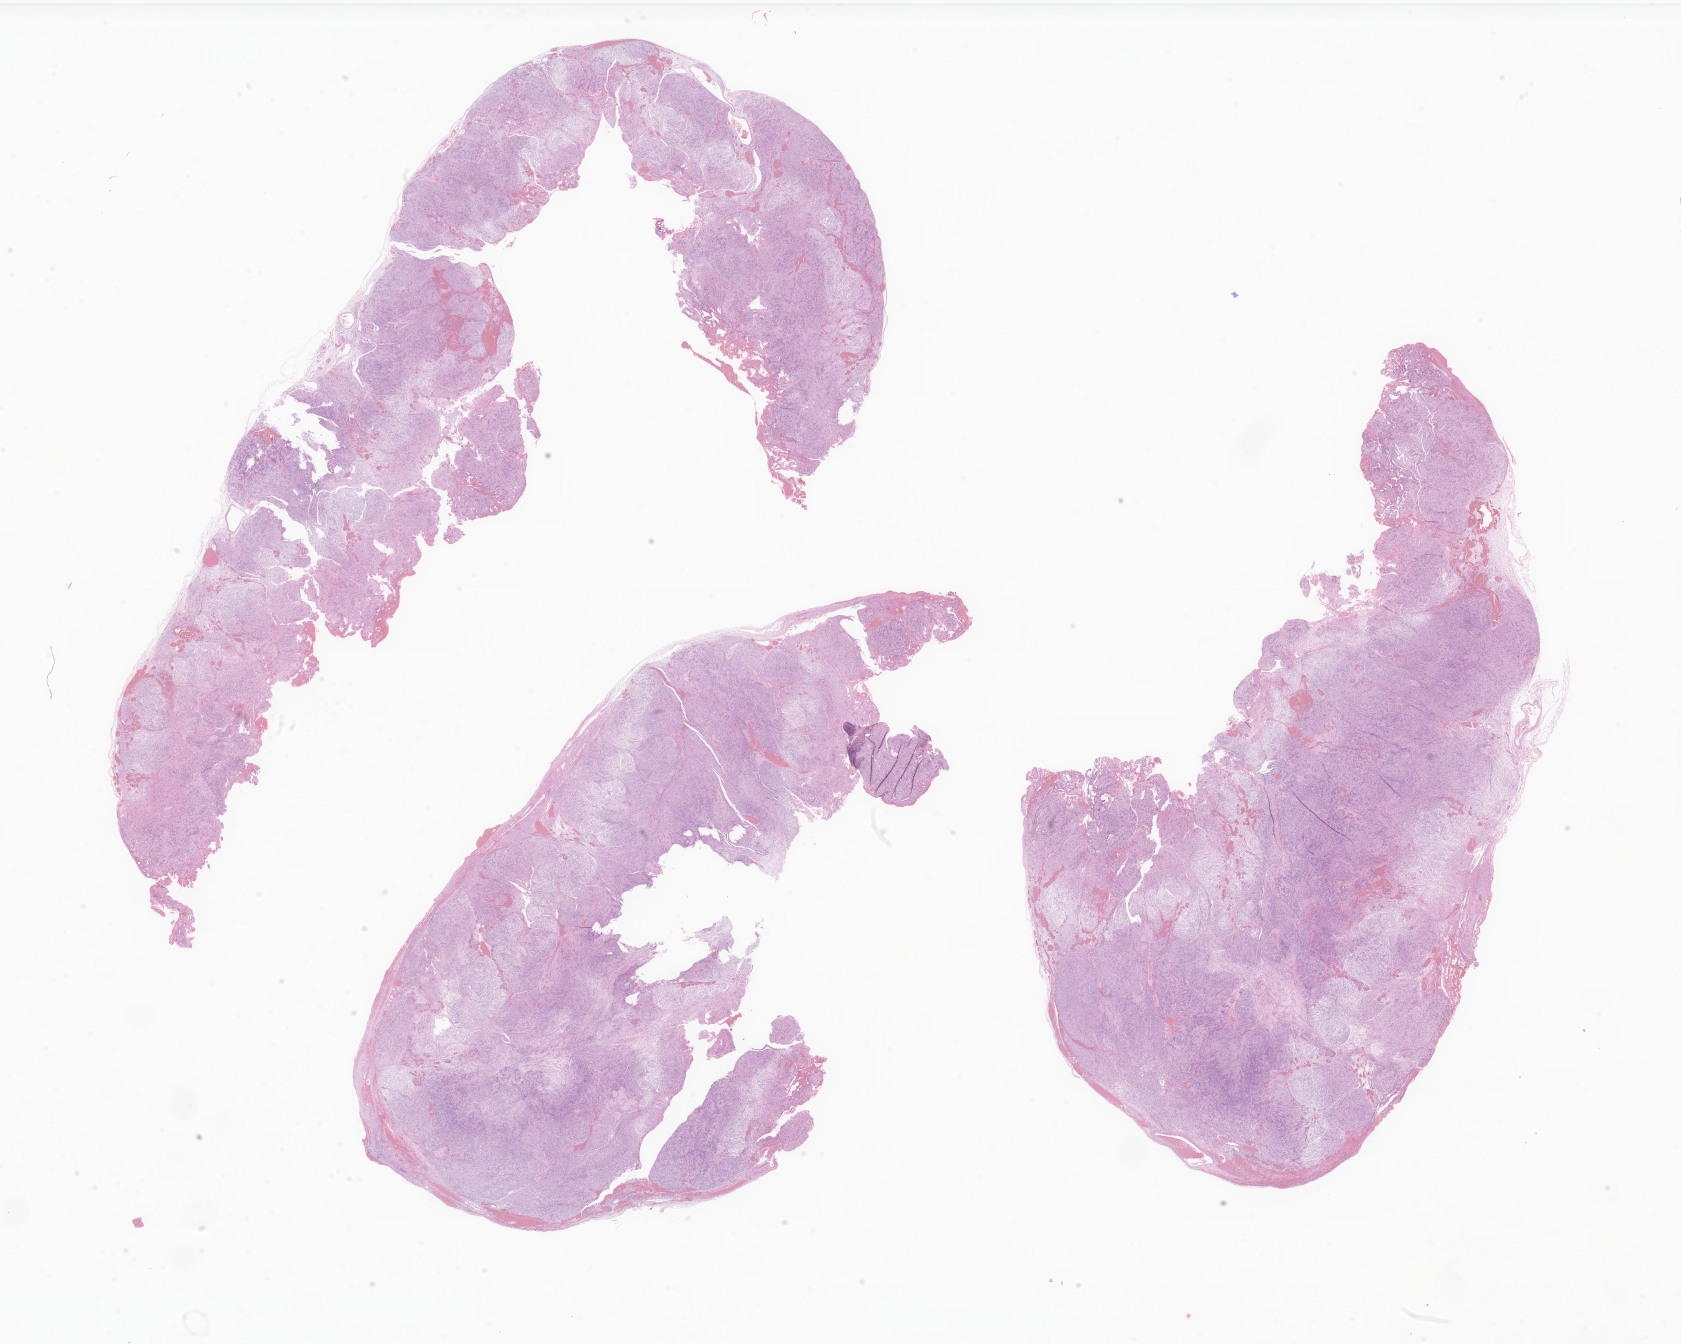
Hematoxylin and eosin (H&E) whole-slide image of tumor tissue from the brain — a low-resolution overview of the entire scanned area, about 28.4 x 22.7 mm, formalin-fixed, paraffin-embedded (FFPE) tissue. Male patient, age 135 months (11 years 3 months).
• diagnosis (ICD-O-3 morphology term): Schwannoma, NOS